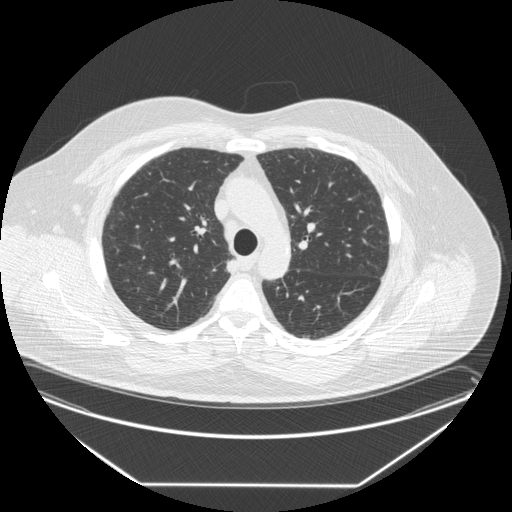
Low-dose screening chest CT, one axial slice. Slice 194 of 258 in the series (ordered by position). Reconstruction kernel STANDARD. 120 kVp. Lung window (W 1500 / L -600 HU). 512 × 512 image matrix, field of view 440 × 440 mm.
Annotated regions visible in this slice (manually delineated by an expert):
- lesion 1 (tumor, upper lobe of right lung): bounding box <227,259,238,274> (left, top, right, bottom; pixels)